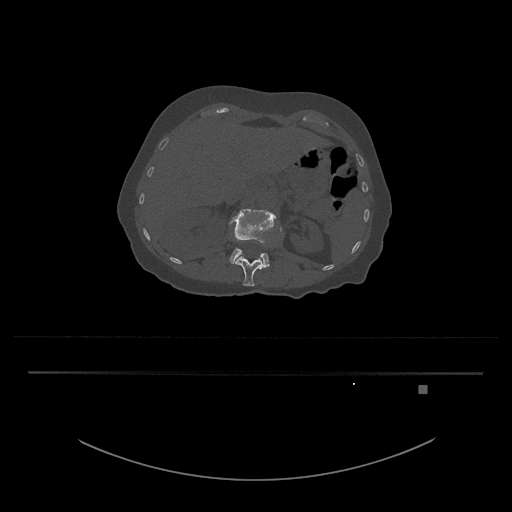
CT including the spine, one axial slice. 120 kVp. Bone window (W 1800 / L 400 HU). 0.5 mm slice thickness. 512 × 512 image matrix, field of view 500 × 500 mm. Patient: female, 57 years. From the clinical record (not read from this slice): primary cancer: cervical.
Structures marked on this image (semi-automatically segmented with operator editing):
- L1 vertebra: bounding box <234,227,283,287> (left, top, right, bottom; pixels)